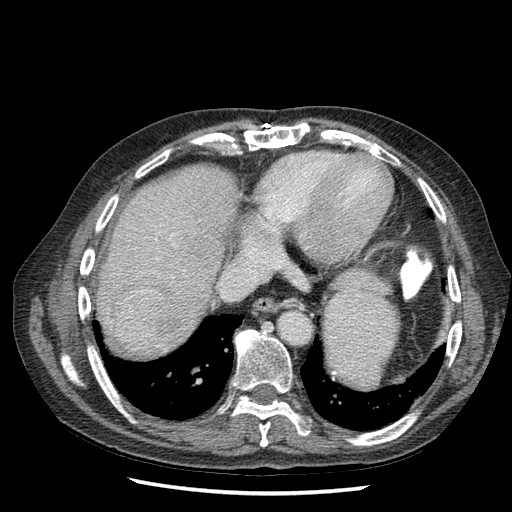
Contrast-enhanced abdominal CT (liver protocol), one axial slice. Position 59 of 67 along the scan axis. Reconstruction kernel STANDARD. 120 kVp. Soft-tissue window (W 400 / L 40 HU). 2.5 mm slice thickness. 512 × 512 image matrix, field of view 360 × 360 mm. From the clinical record (not read from this slice): diagnosis: hepatocellular carcinoma (patient treated with transarterial chemoembolisation; whether this scan precedes or follows treatment is not stated here); TNM stage (as recorded): Stage-I; Child-Pugh class: A; tumour differentiation: moderately differentiated; tumour nodularity: uninodular.
Annotated regions visible in this slice (semi-automatically segmented with operator editing):
- liver parenchyma outside the tumour (the mass and vessels are separate outlines, so this box may not span the whole liver): bounding box [x1, y1, x2, y2] px = [104, 167, 230, 348]
- mass: [115, 287, 181, 345]
- liver vessels: [168, 279, 174, 287]